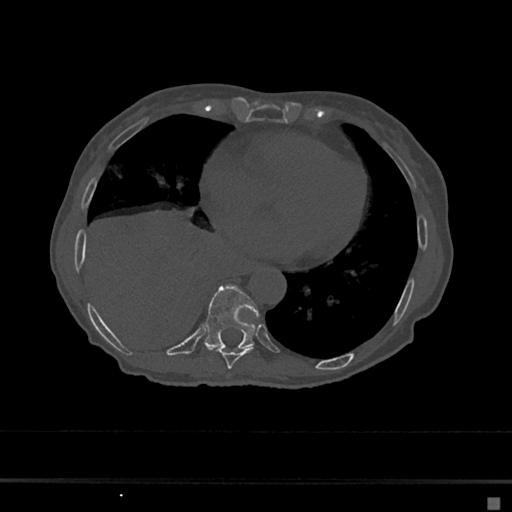
CT including the spine, one axial slice; slice 296 of 797 in the series (ordered by position); bone window (W 1800 / L 400 HU); 0.5 mm slice thickness; 512 × 512 image matrix, field of view 360 × 360 mm. Patient: female, 68 years. Case-level facts recorded for this patient, not image findings: primary cancer: renal.
Structures marked on this image (semi-automatically segmented with operator editing):
- T8 vertebra: box from (x=215, y=347) to (x=254, y=369) px
- T9 vertebra: (x=203, y=285)–(x=259, y=349)